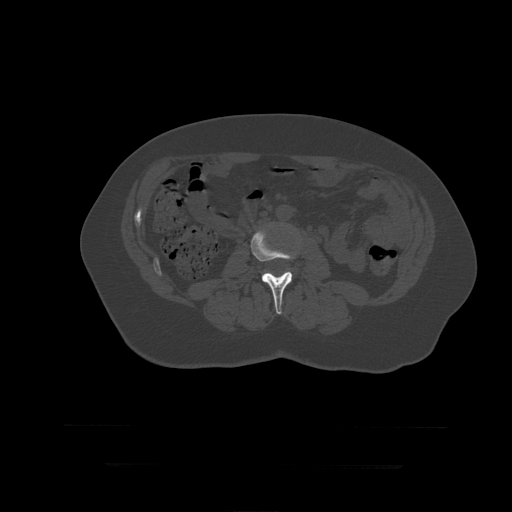
CT including the spine, one axial slice. Slice 117 of 399 in the series (ordered by position). Bone window (W 1800 / L 400 HU). 512 × 512 image matrix, field of view 450 × 450 mm. Patient age 41 years. From the clinical record (not read from this slice): primary cancer: breast.
Structures marked on this image (semi-automatic segmentation, software-assisted and operator-edited):
- L3 vertebra: bounding box (x1, y1, x2, y2) in pixels: (251, 230, 296, 315)